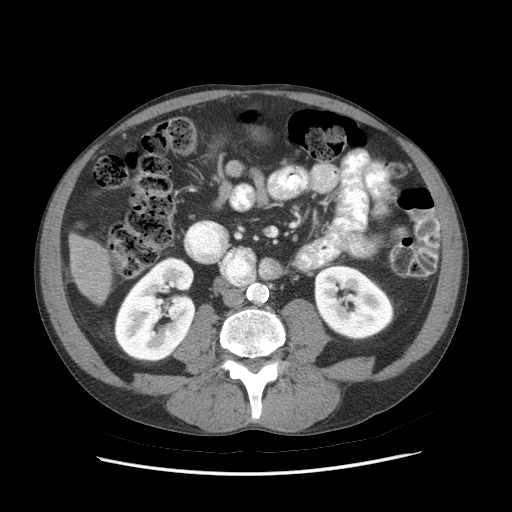
Contrast-enhanced abdominal CT (liver protocol), one axial slice. Position 13 of 89 along the scan axis. Reconstruction kernel STANDARD. Soft-tissue window (W 400 / L 40 HU). 2.5 mm slice thickness. 512 × 512 image matrix, field of view 380 × 380 mm. Case-level facts recorded for this patient, not image findings: diagnosis: hepatocellular carcinoma (patient treated with transarterial chemoembolisation; whether this scan precedes or follows treatment is not stated here); TNM stage (as recorded): Stage-IIIB; Child-Pugh class: A; tumour differentiation: moderately differentiated.
Outlined on this slice (semi-automatically segmented with operator editing):
- liver parenchyma outside the tumour (the mass and vessels are separate outlines, so this box may not span the whole liver): bounding box <68,234,112,302> (left, top, right, bottom; pixels)